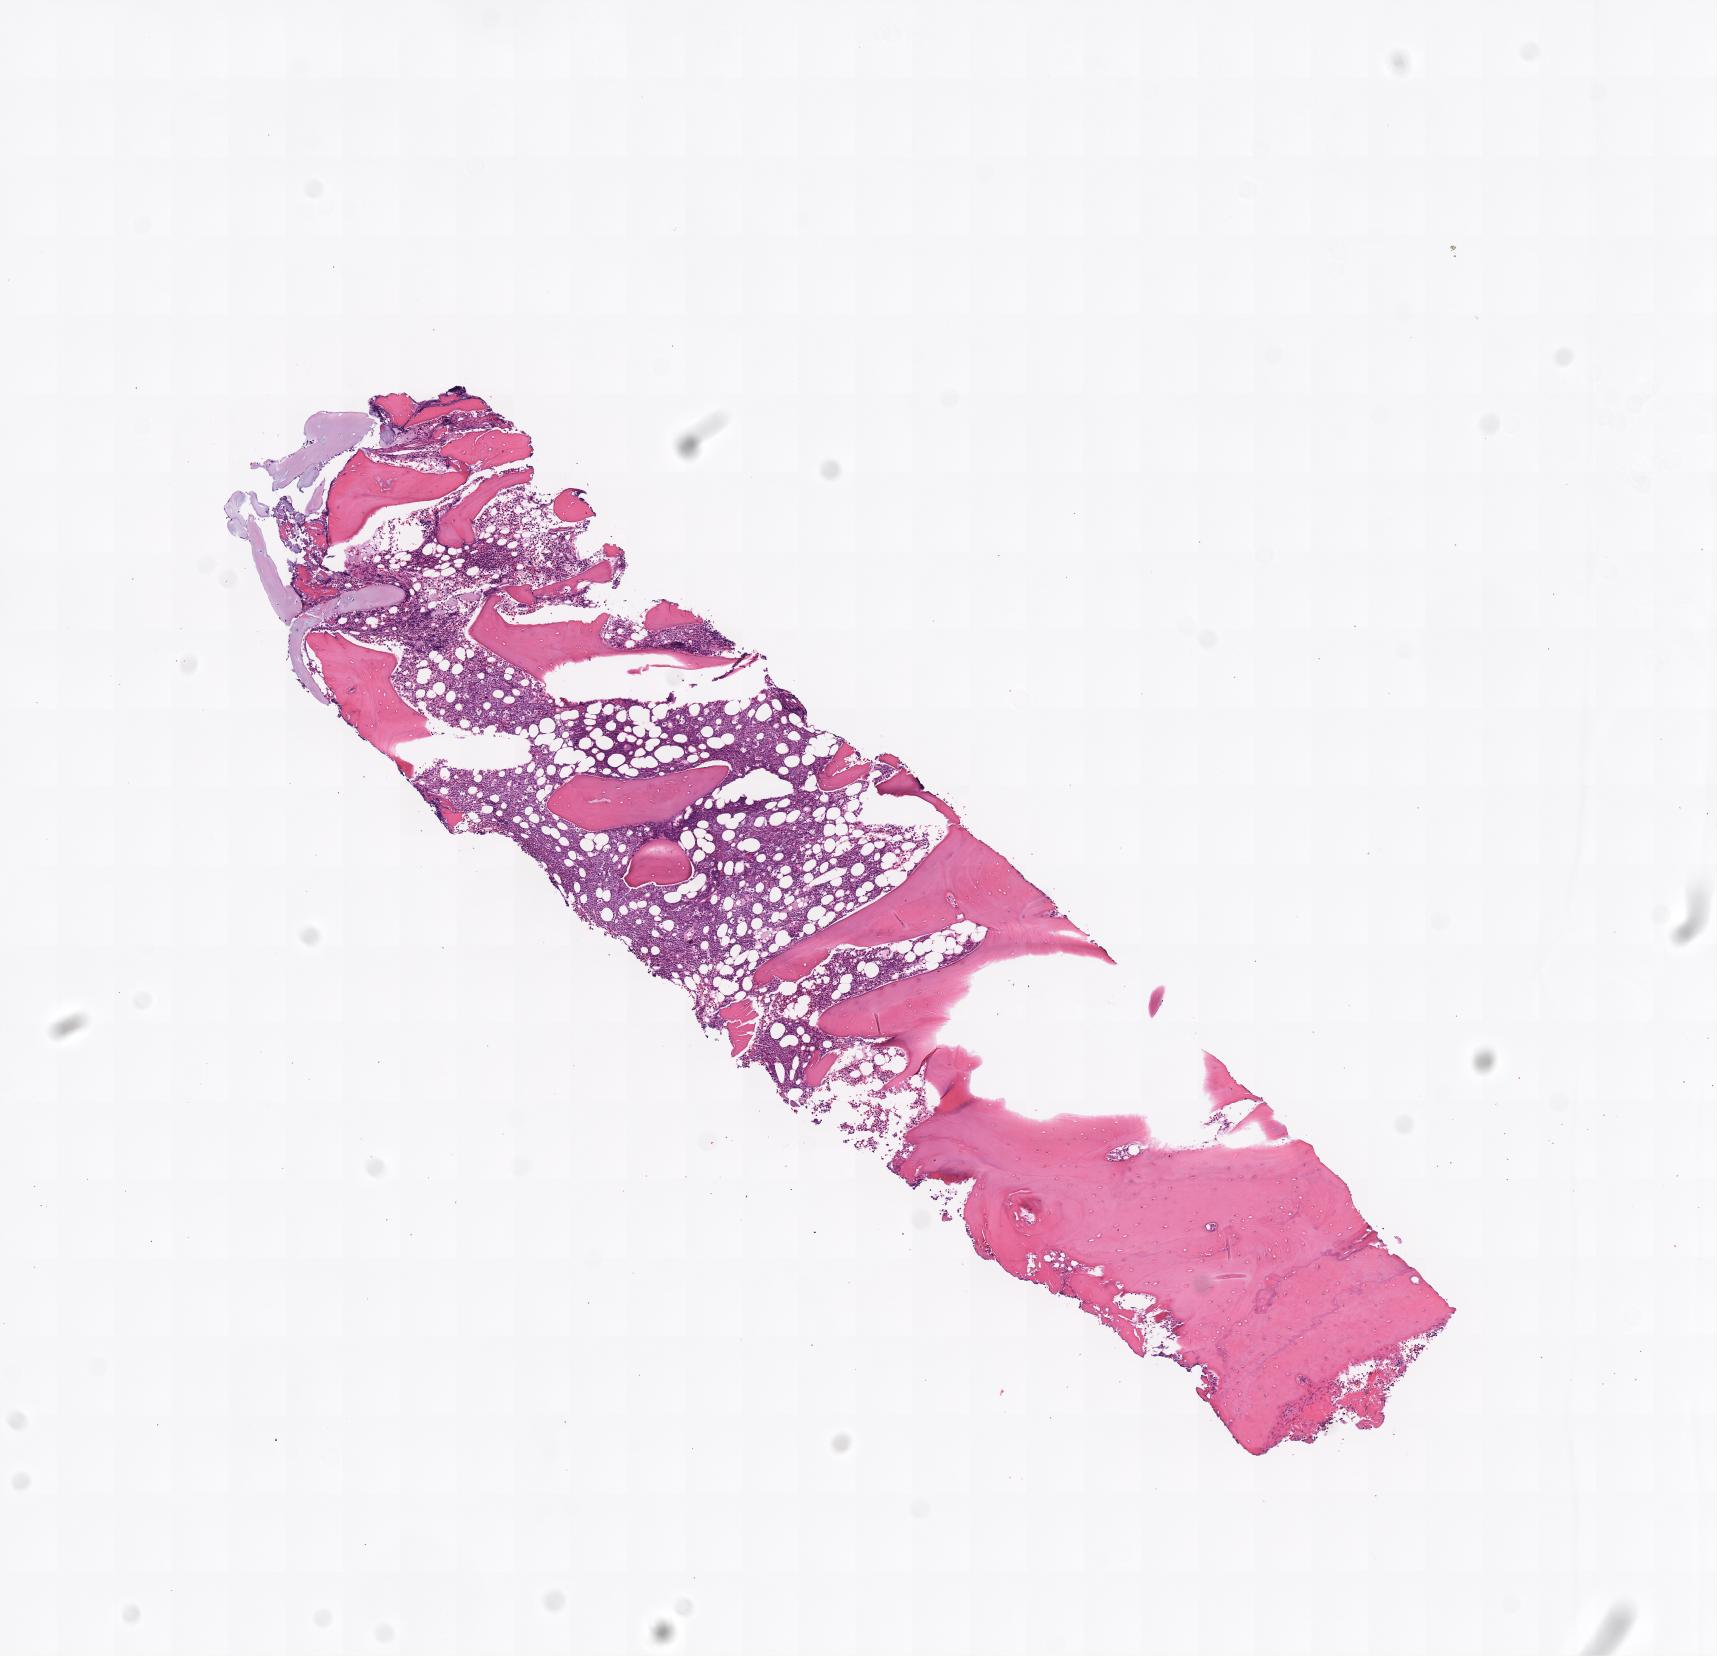
Hematoxylin and eosin (H&E) whole-slide image — low-resolution overview of the scanned area, specimen: tumor tissue, site: bone marrow. Female patient; age at initial diagnosis 4 years.
Diagnosis: Burkitt lymphoma, NOS.